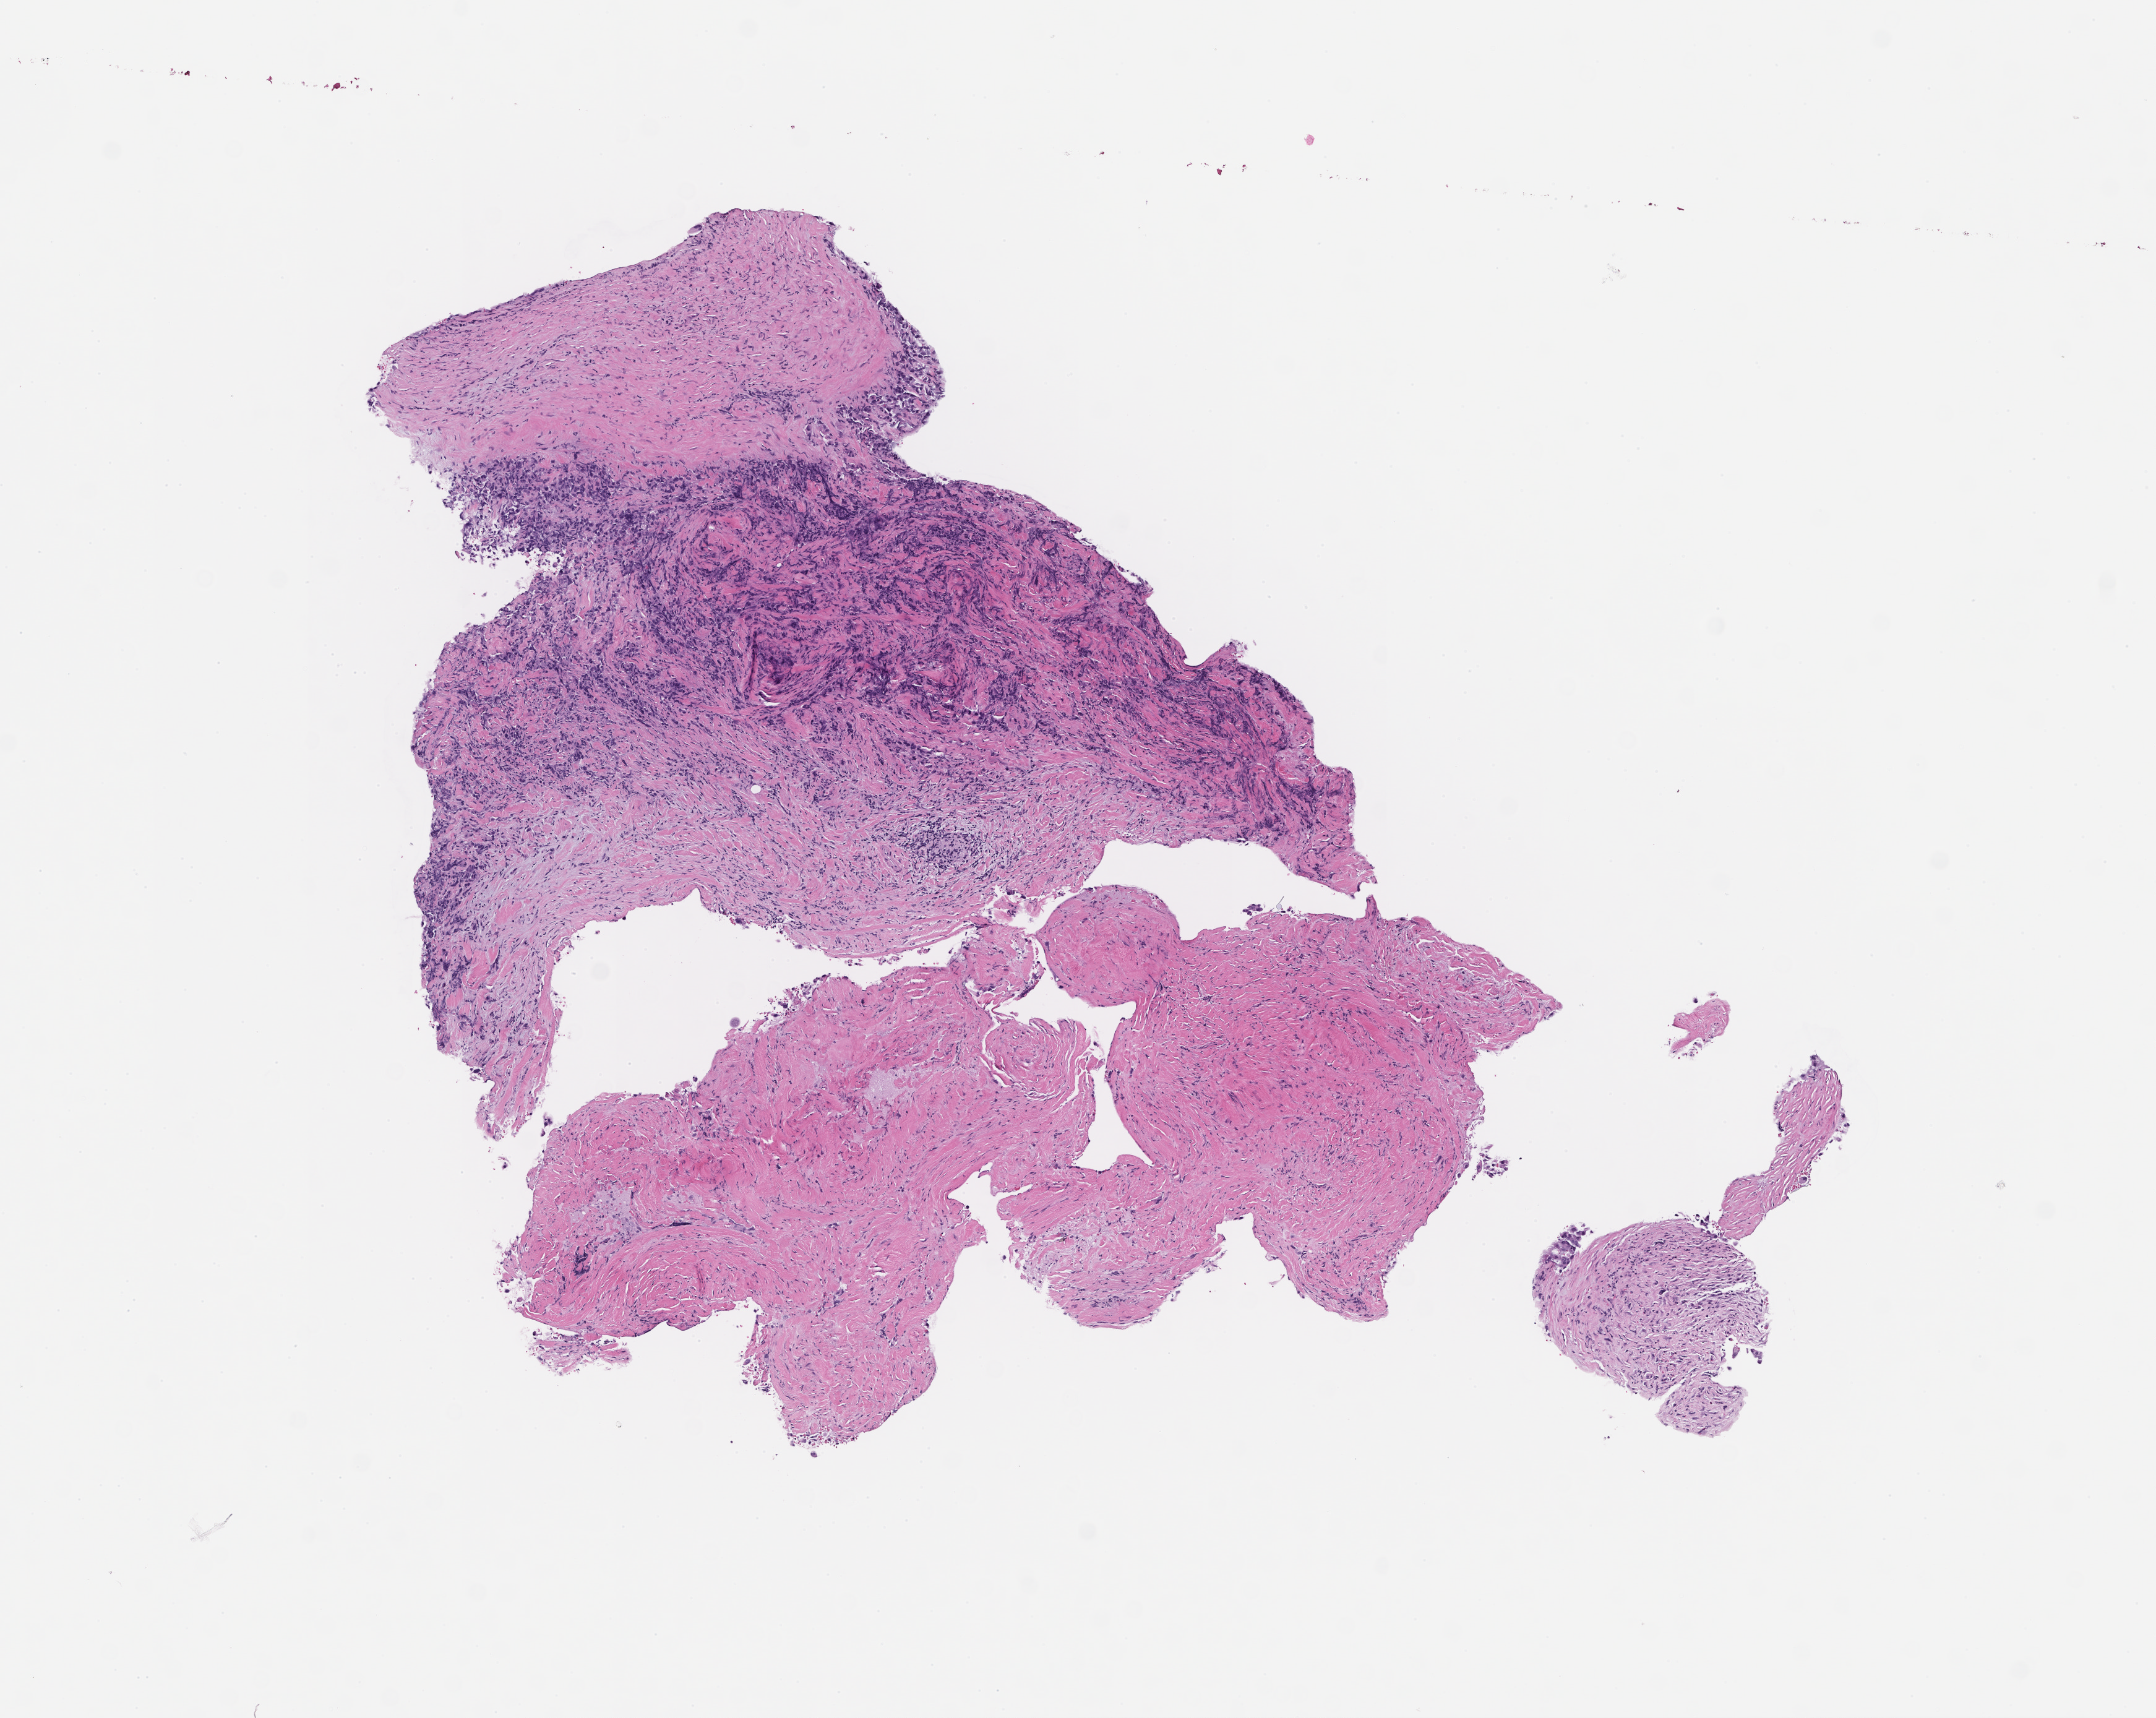
Digitized hematoxylin and eosin (H&E)-stained section — low-resolution overview of the scanned area, about 7.0 x 5.6 mm. FFPE section. Site: lung. Specimen time point: collected at baseline (before treatment). Patient: male.
This section: primary tumour tissue. Diagnosis: Non-Small Cell Lung Carcinoma.